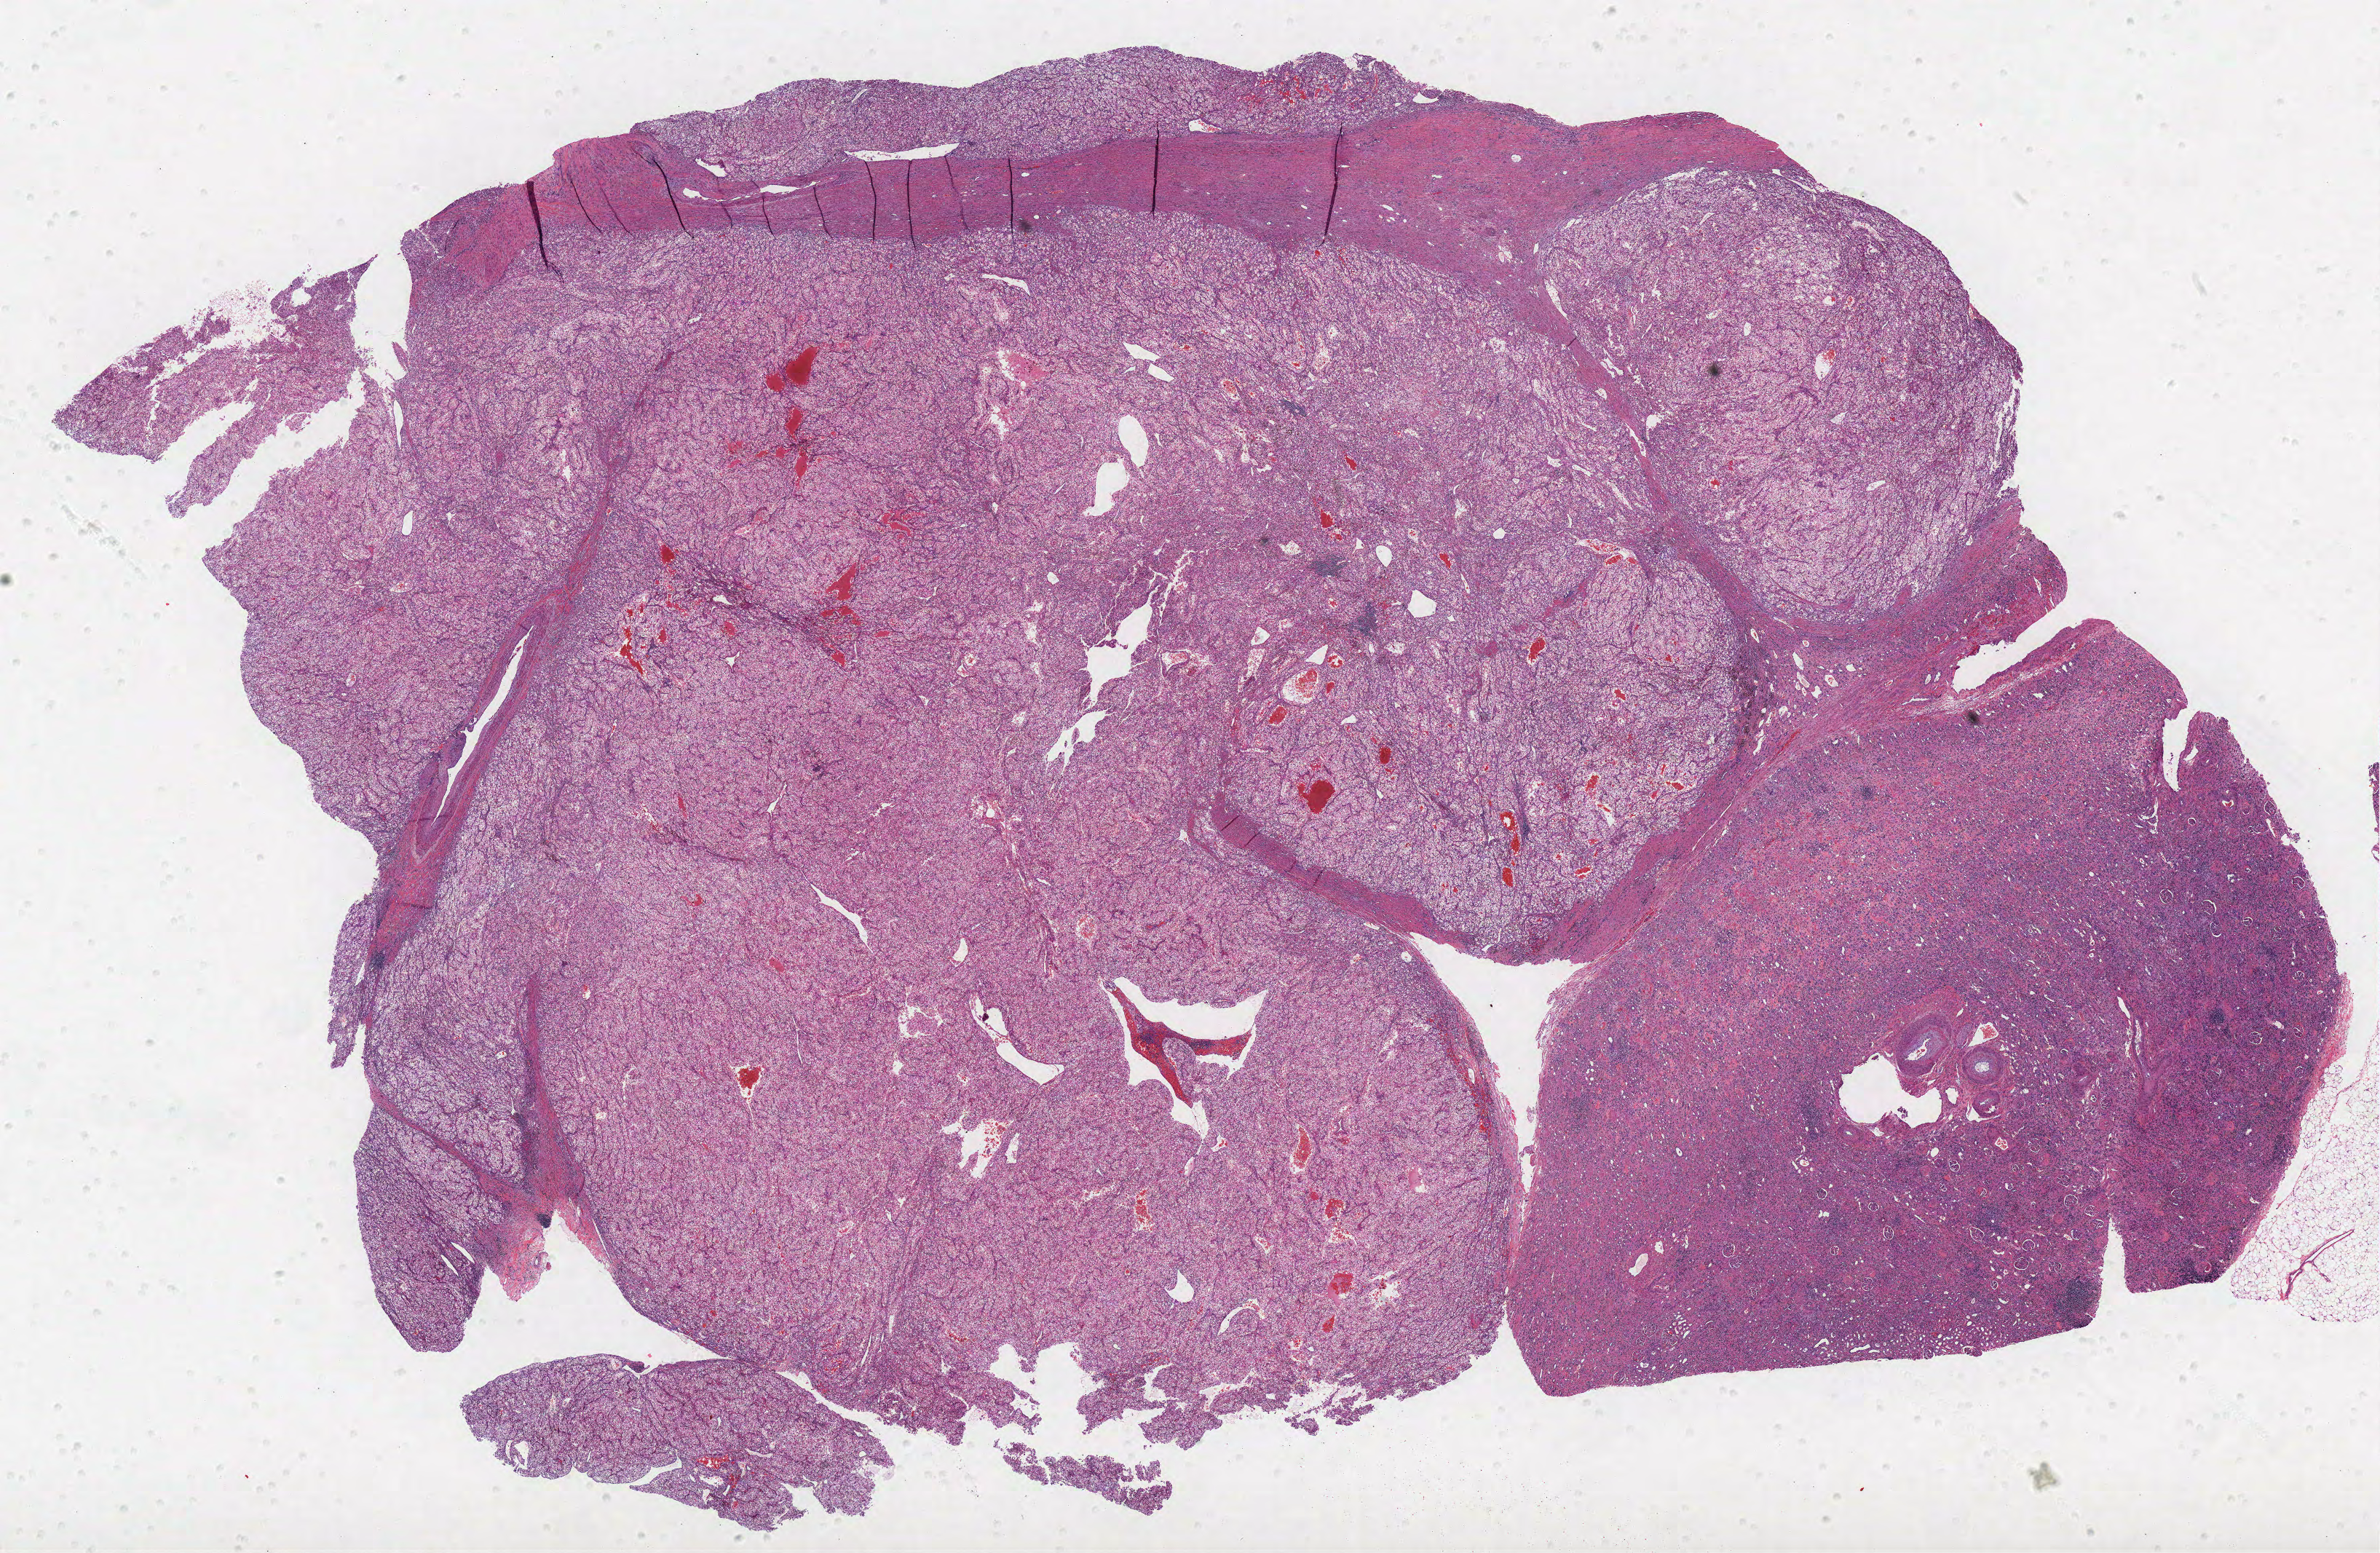
Whole-slide histology image, H&E-stained, shown as a low-resolution overview of the whole scanned area (about 26.1 x 17.1 mm, slide scanned at 40x), FFPE section, sample: primary tumour, kidney. Male, age 71 years at initial diagnosis.
Pathologic diagnosis: Clear cell adenocarcinoma, NOS.